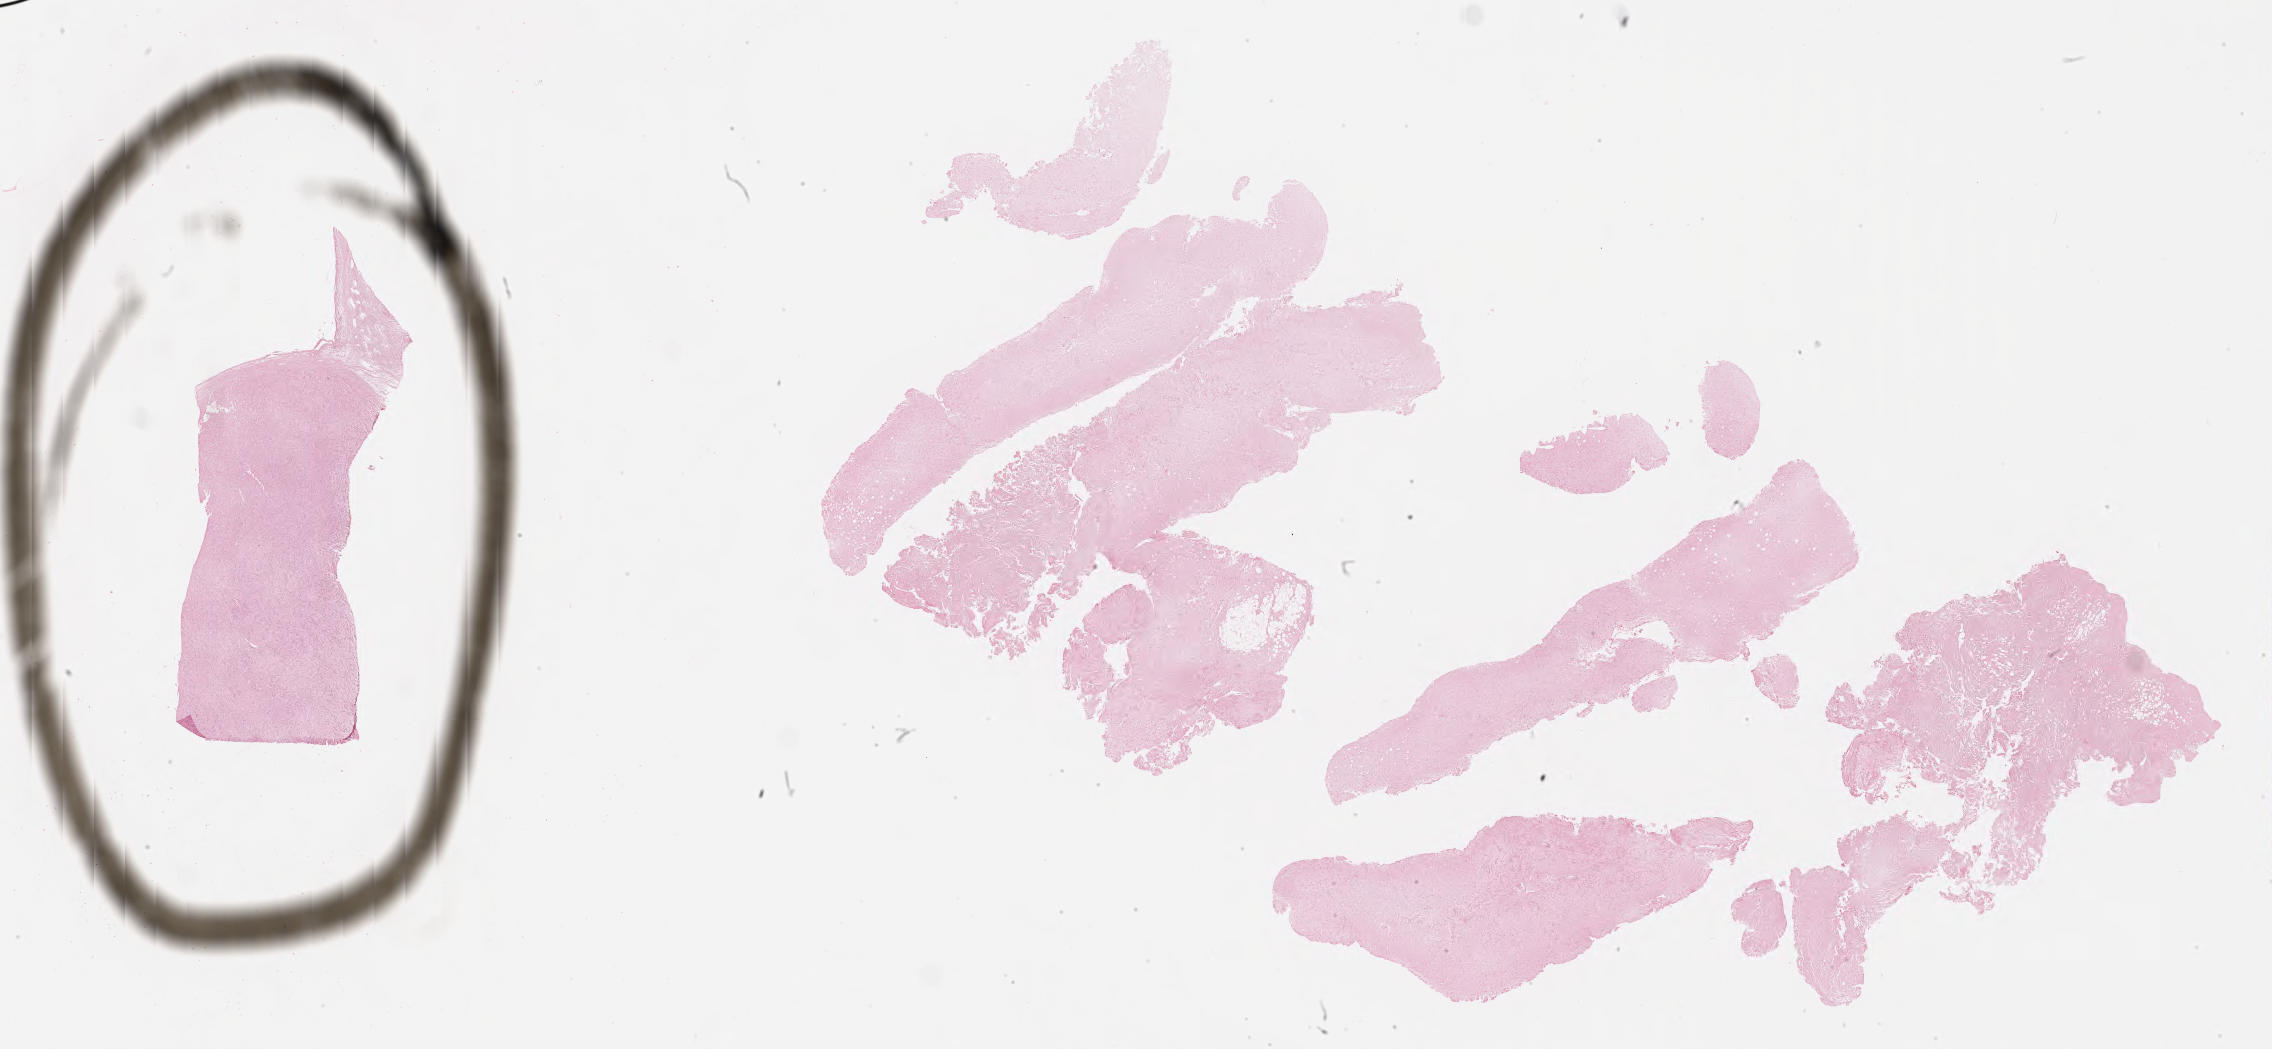
Whole-slide image, Epstein–Barr virus-encoded RNA (EBER) in-situ hybridisation, a low-resolution overview of the entire scanned area, about 36.7 x 17.0 mm; tumor tissue. Patient male; 45 years old.
Diagnosis: Diffuse large B-cell lymphoma, NOS.